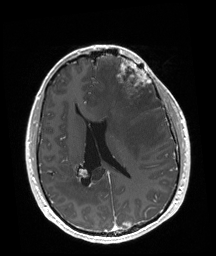
Brain MRI from a brain-tumour surgery series, one axial slice; slice 78 of 192 in the series (ordered by position); T1-weighted post-contrast; 1 mm slice thickness; 216 × 256 image matrix.
Annotated regions visible in this slice (manually delineated by an expert):
- tumour: box from (x=116, y=59) to (x=151, y=102) px